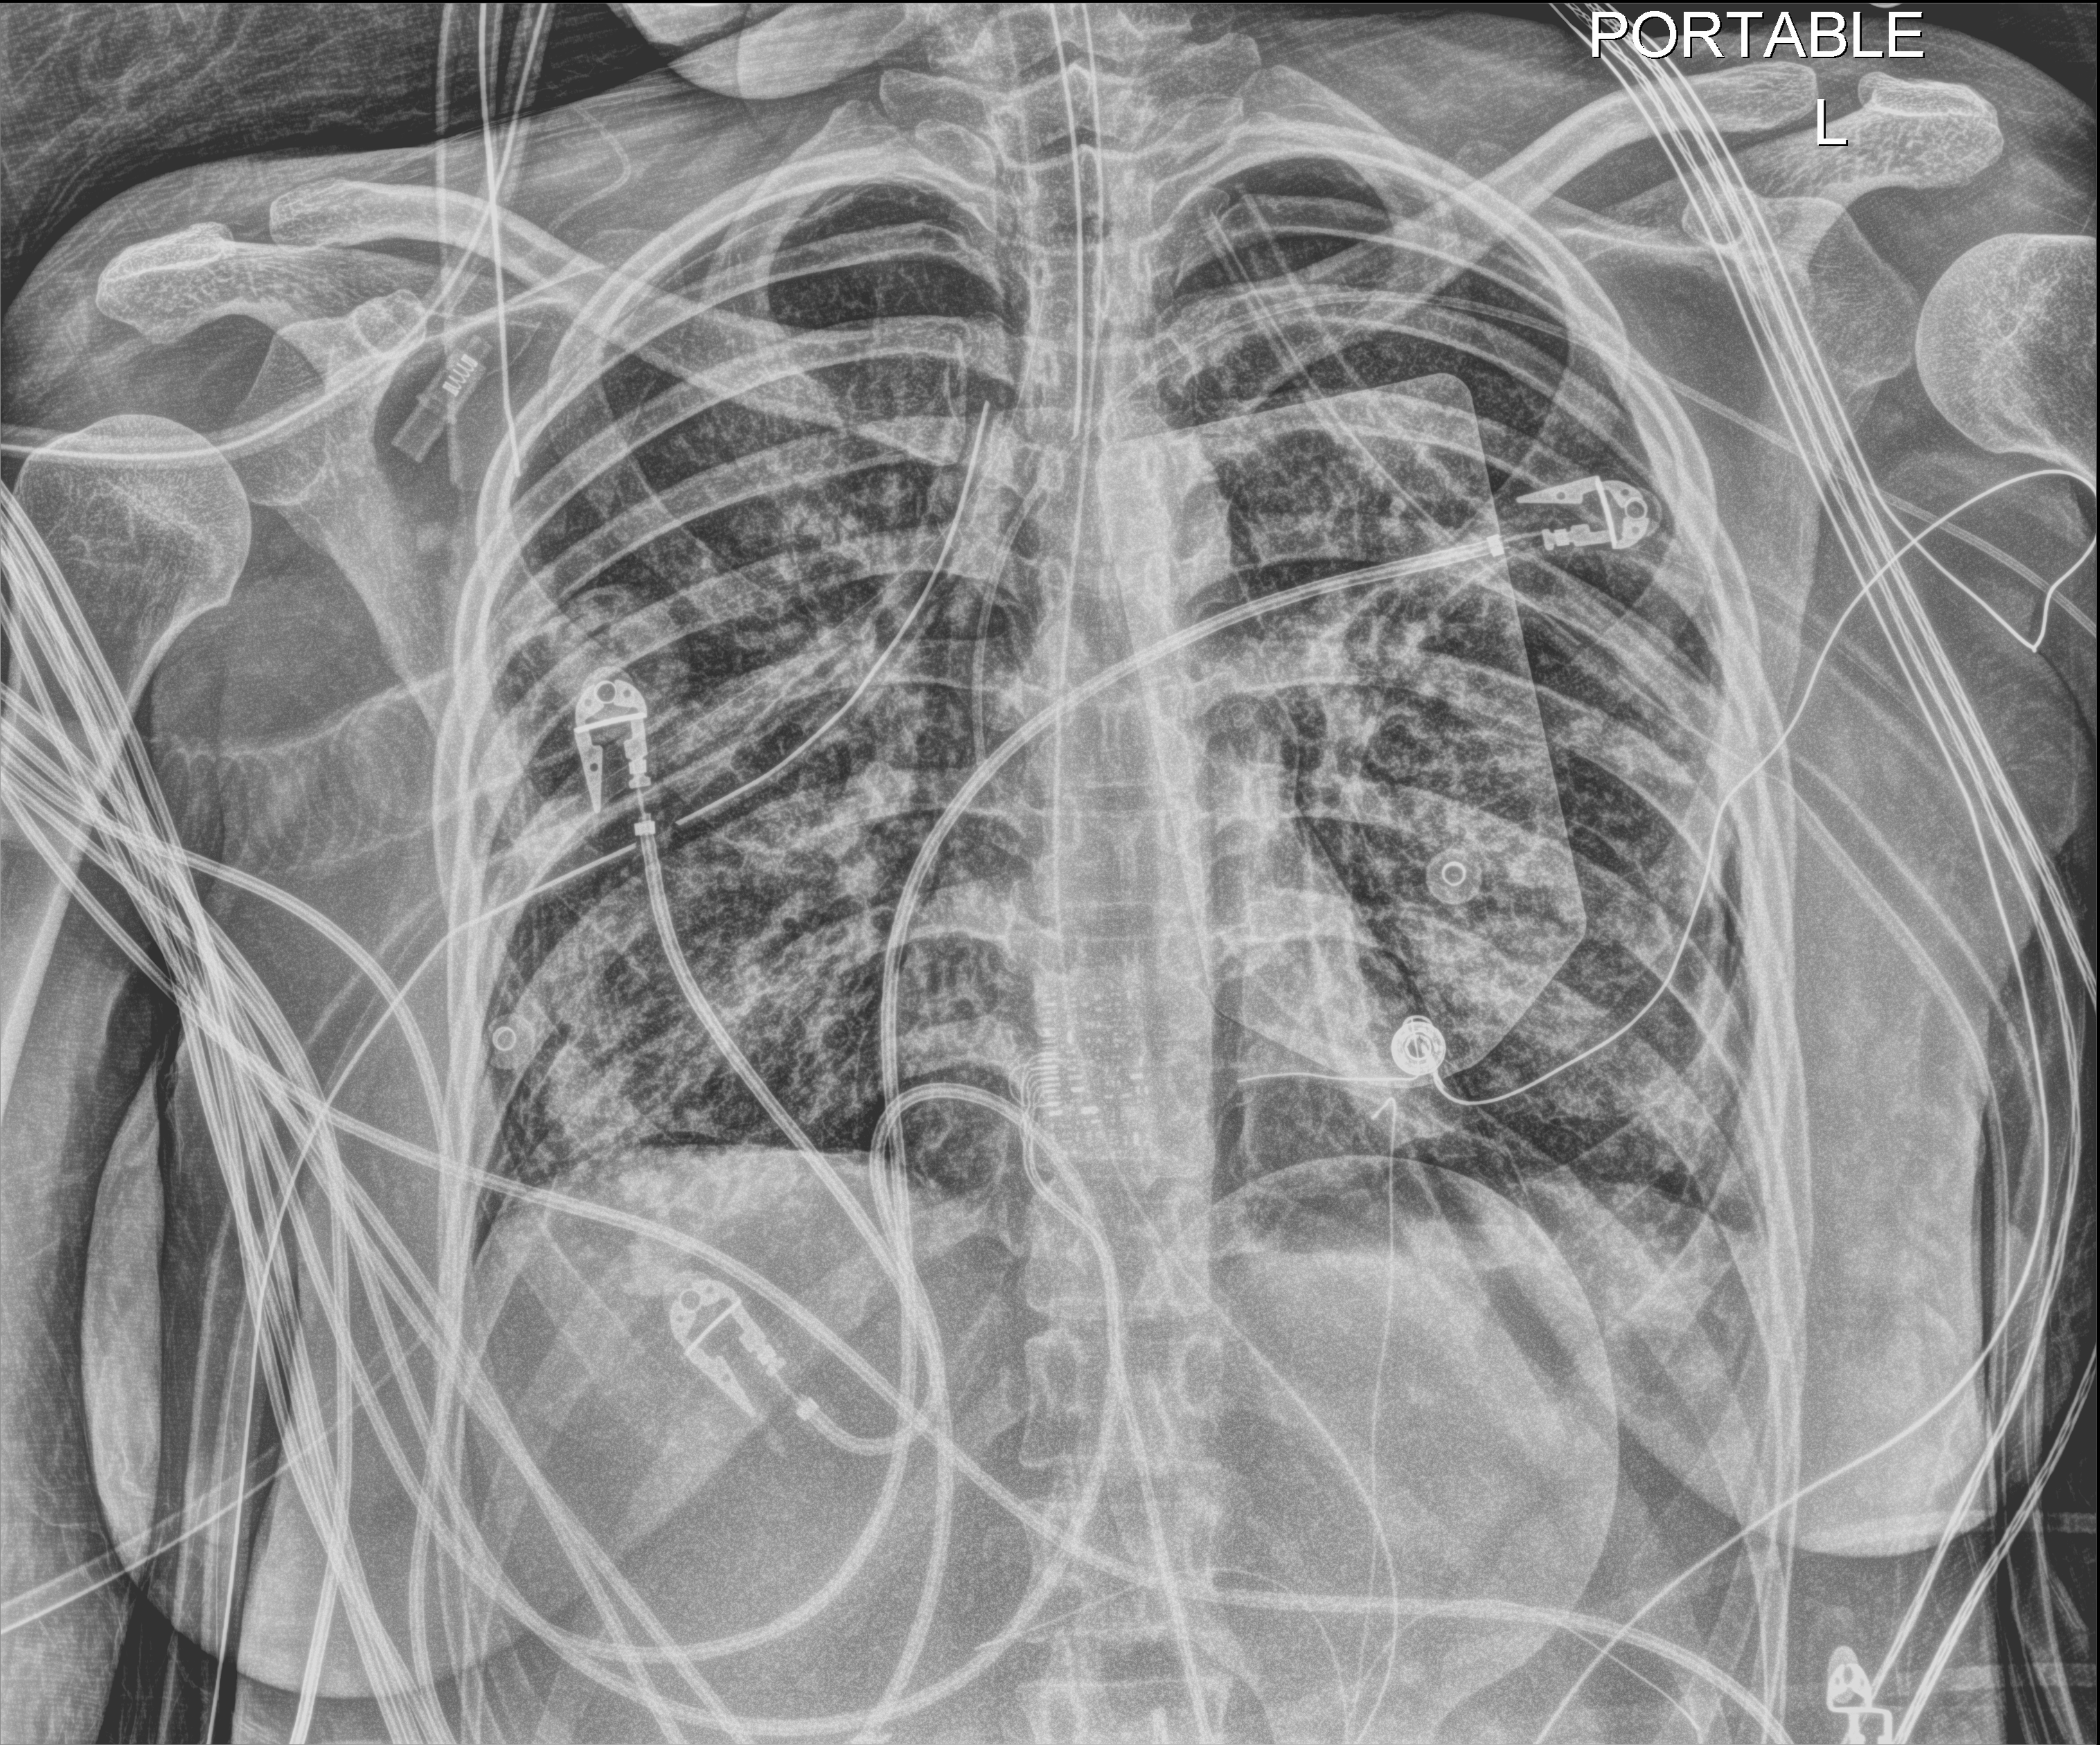
Portable chest radiograph. Adult patient hospitalised with COVID-19, age 18–59 years.
Admission-level facts for this patient (not findings on this image; timing relative to this image not recorded):
- other chronic lung disease (admission record): no